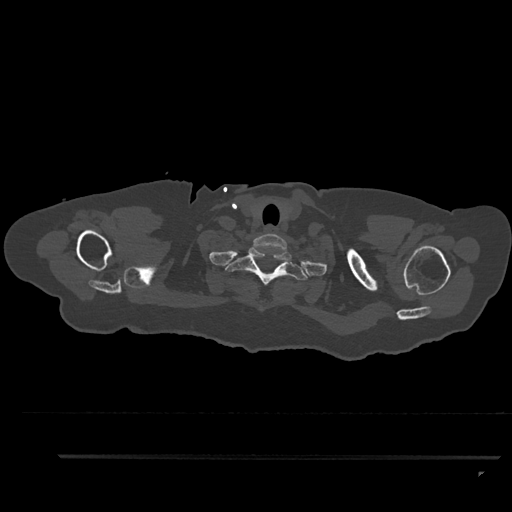
CT including the spine, one axial slice; position 770 of 797 along the scan axis; 120 kVp; bone window (W 1800 / L 400 HU); 0.5 mm slice thickness; 512 × 512 image matrix, field of view 408 × 408 mm. Female patient, age 44 years. Case-level facts recorded for this patient, not image findings: primary cancer: renal; vertebrae with lytic lesions (as recorded): L1.
Annotated regions visible in this slice (semi-automatically segmented with operator editing):
- T1 vertebra: bounding box <225,246,309,285> (left, top, right, bottom; pixels)